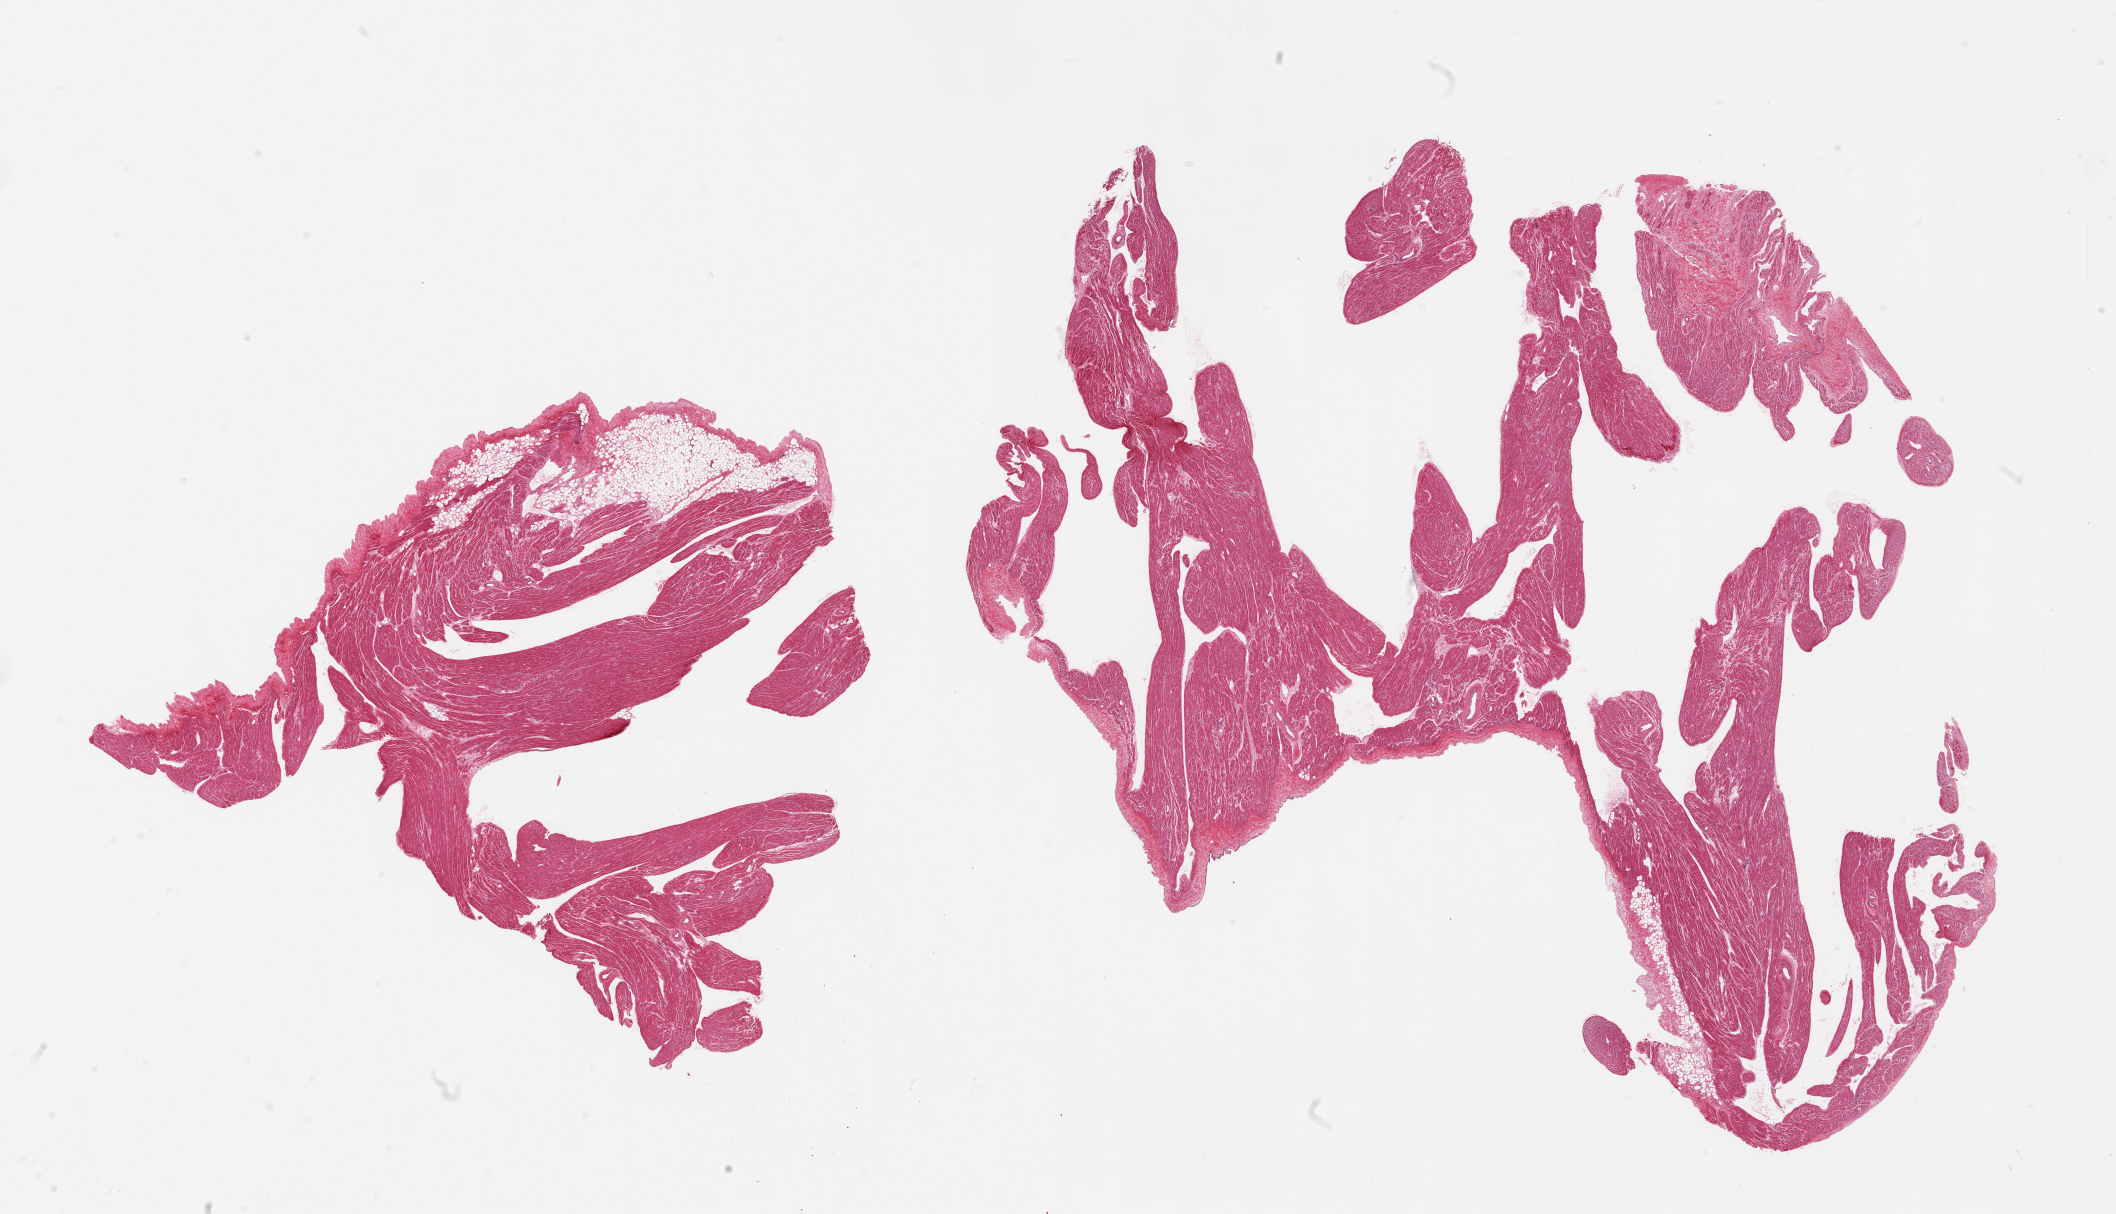
Whole-slide image, H&E stain, a low-resolution overview of the entire scanned area, about 33.5 x 19.2 mm (slide scanned at 20x); PAXgene-fixed paraffin-embedded (PFPE) section; target tissue: auricular appendage; donor tissue sample. Donor sex: male.
Pathologist's review note for this sample: 2 pieces; 25% external fat in 1 piece.